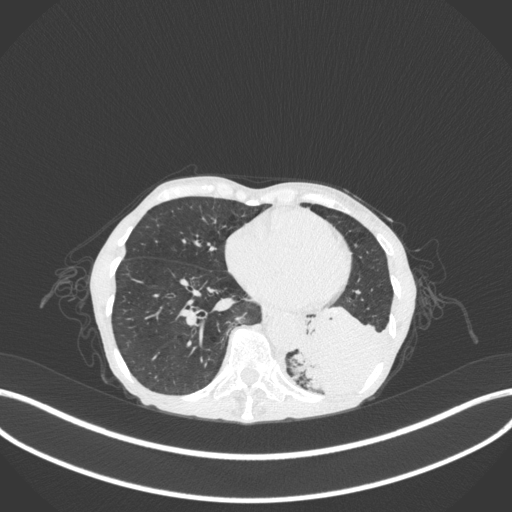
Chest CT, one axial slice; position 87 of 347 along the scan axis; lung window (W 1500 / L -600 HU); 1 mm slice thickness; 512 × 512 image matrix, field of view 400 × 400 mm. Female patient, age 70 years. From the clinical record (not read from this slice): clinical TNM (as recorded): T3 N0 M0; histopathological grade: G3.
Outlined on this slice (rectangle marked by the reading radiologist):
- lung tumour (recorded histology: small cell carcinoma): box from (x=294, y=298) to (x=390, y=407) px